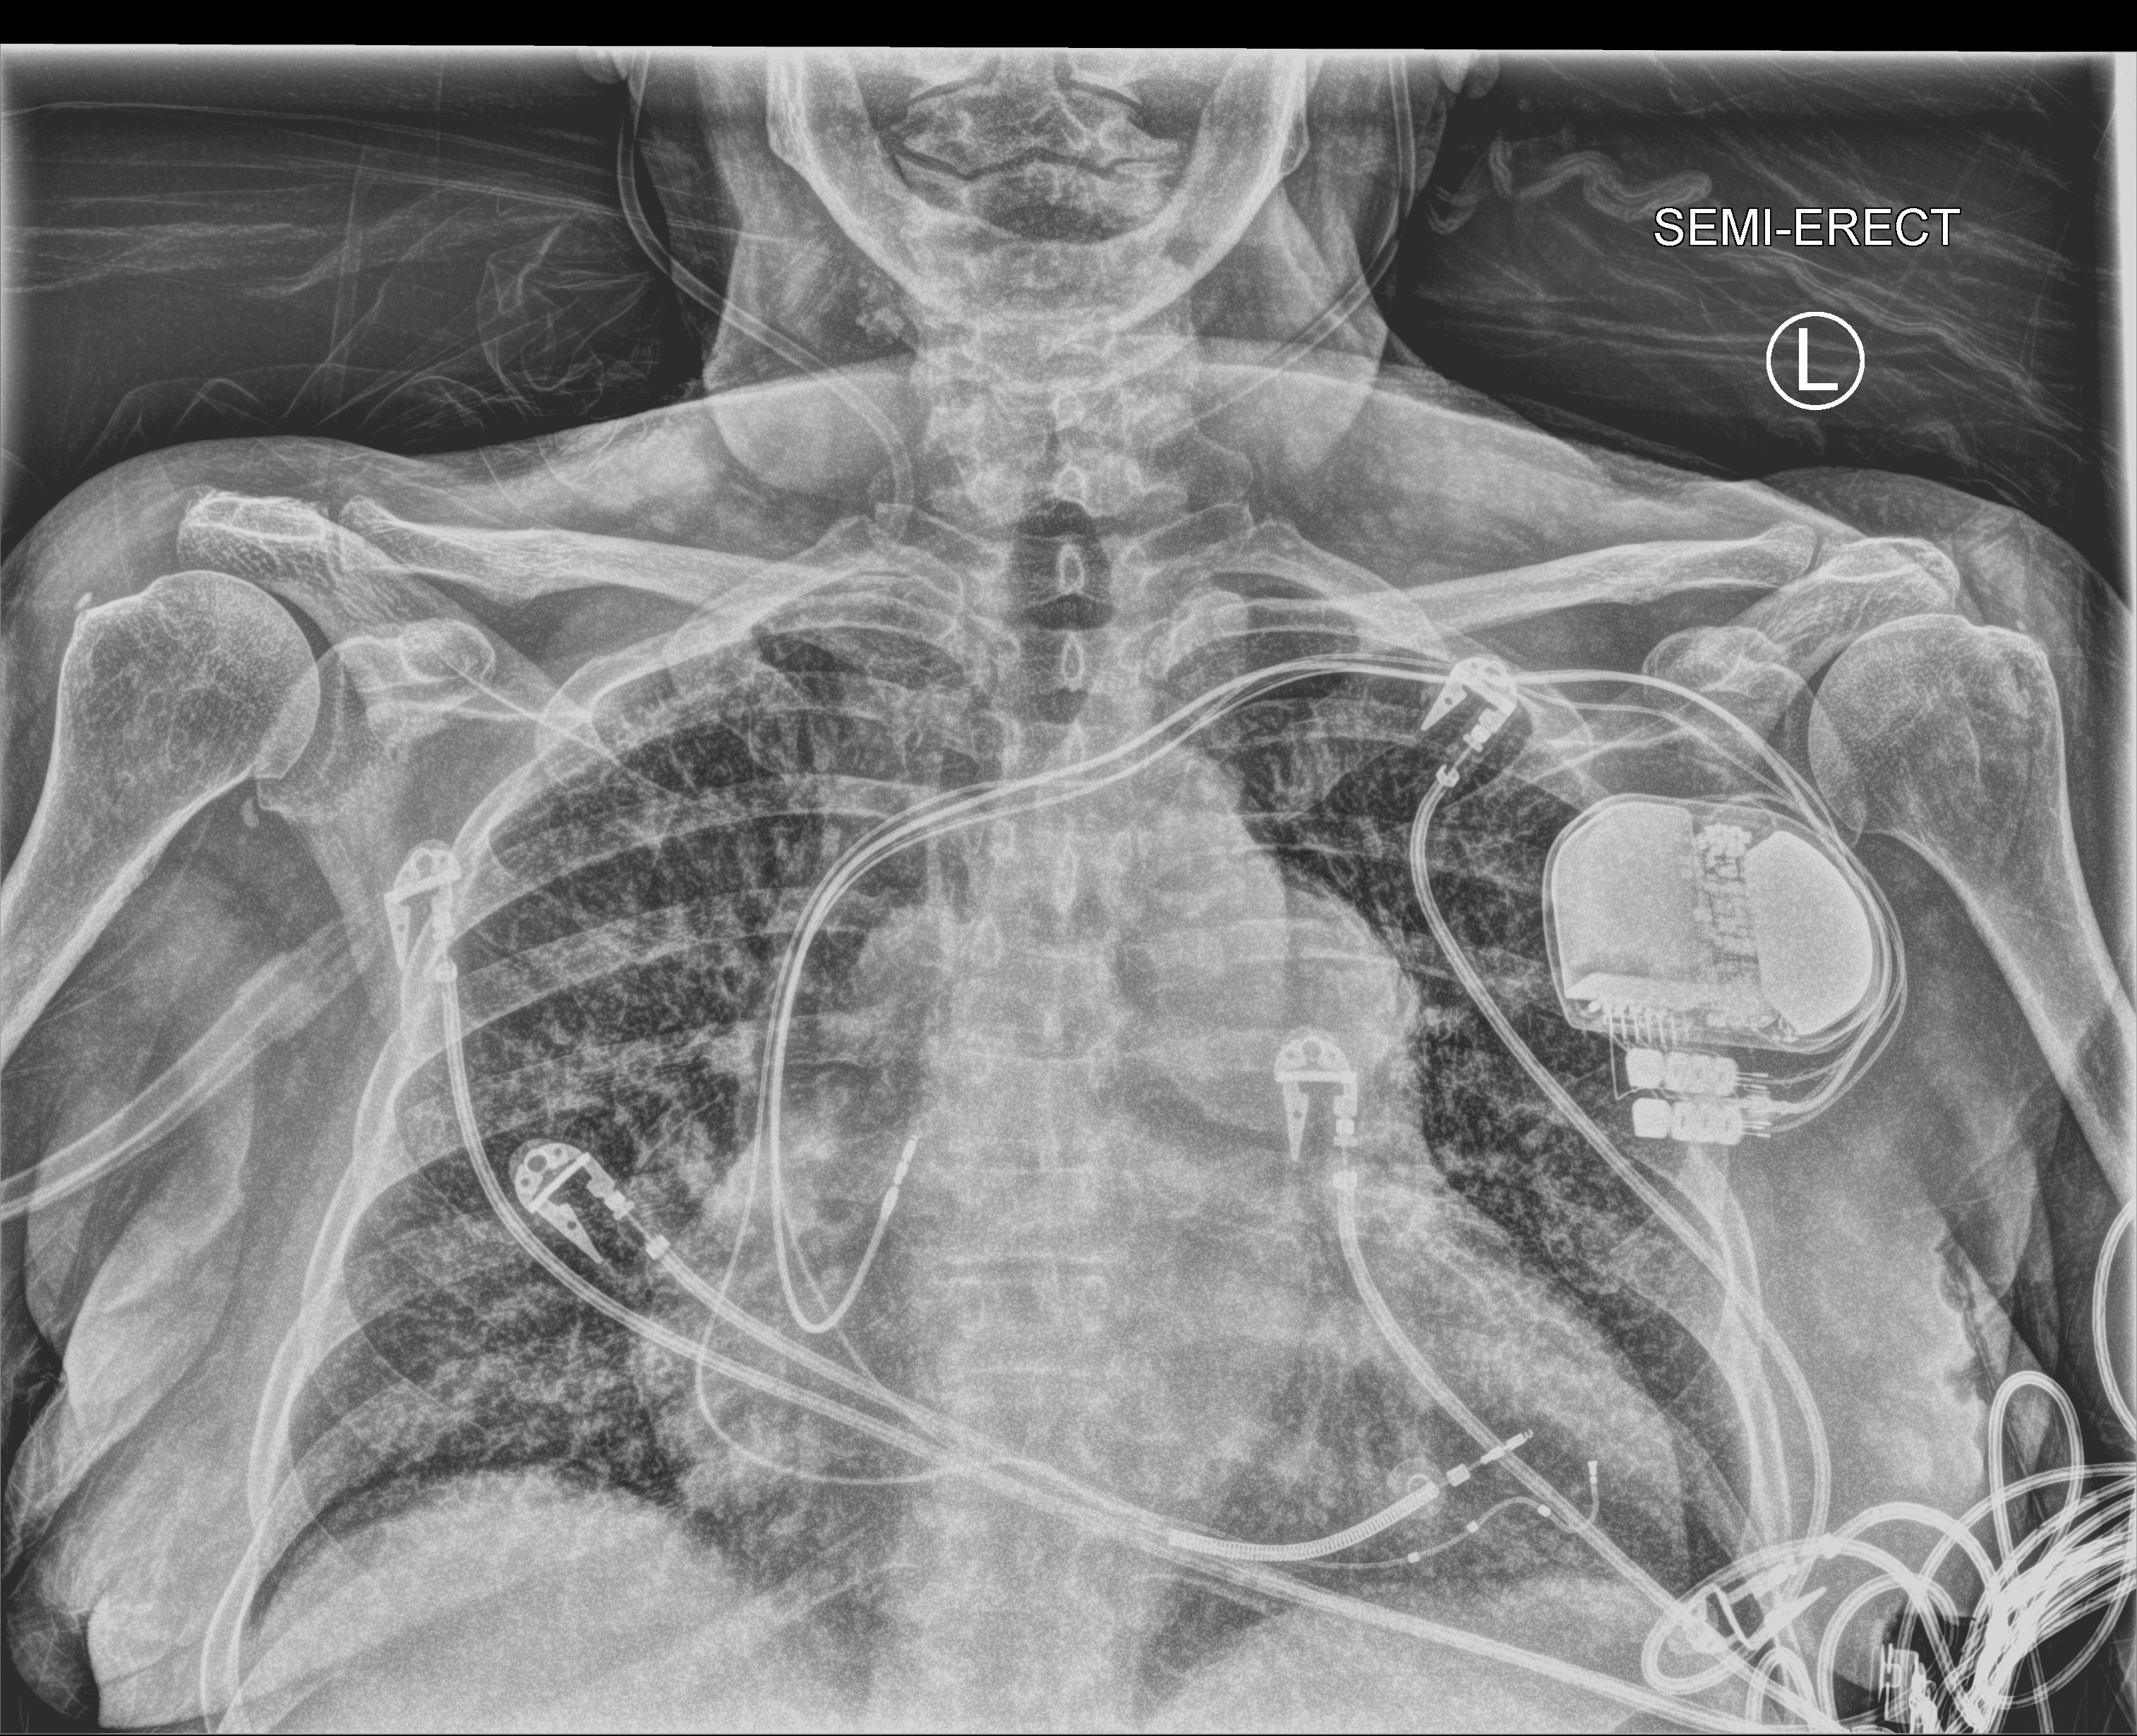
Portable chest radiograph, anteroposterior (AP) projection. Patient hospitalised with COVID-19; female, aged 60–74 years.
Hospital-stay facts (about this admission, not read from this image; timing relative to this image not recorded): admitted to intensive care during this hospital stay: yes; mechanically ventilated during this hospital stay: no; length of hospital stay: 6 days.